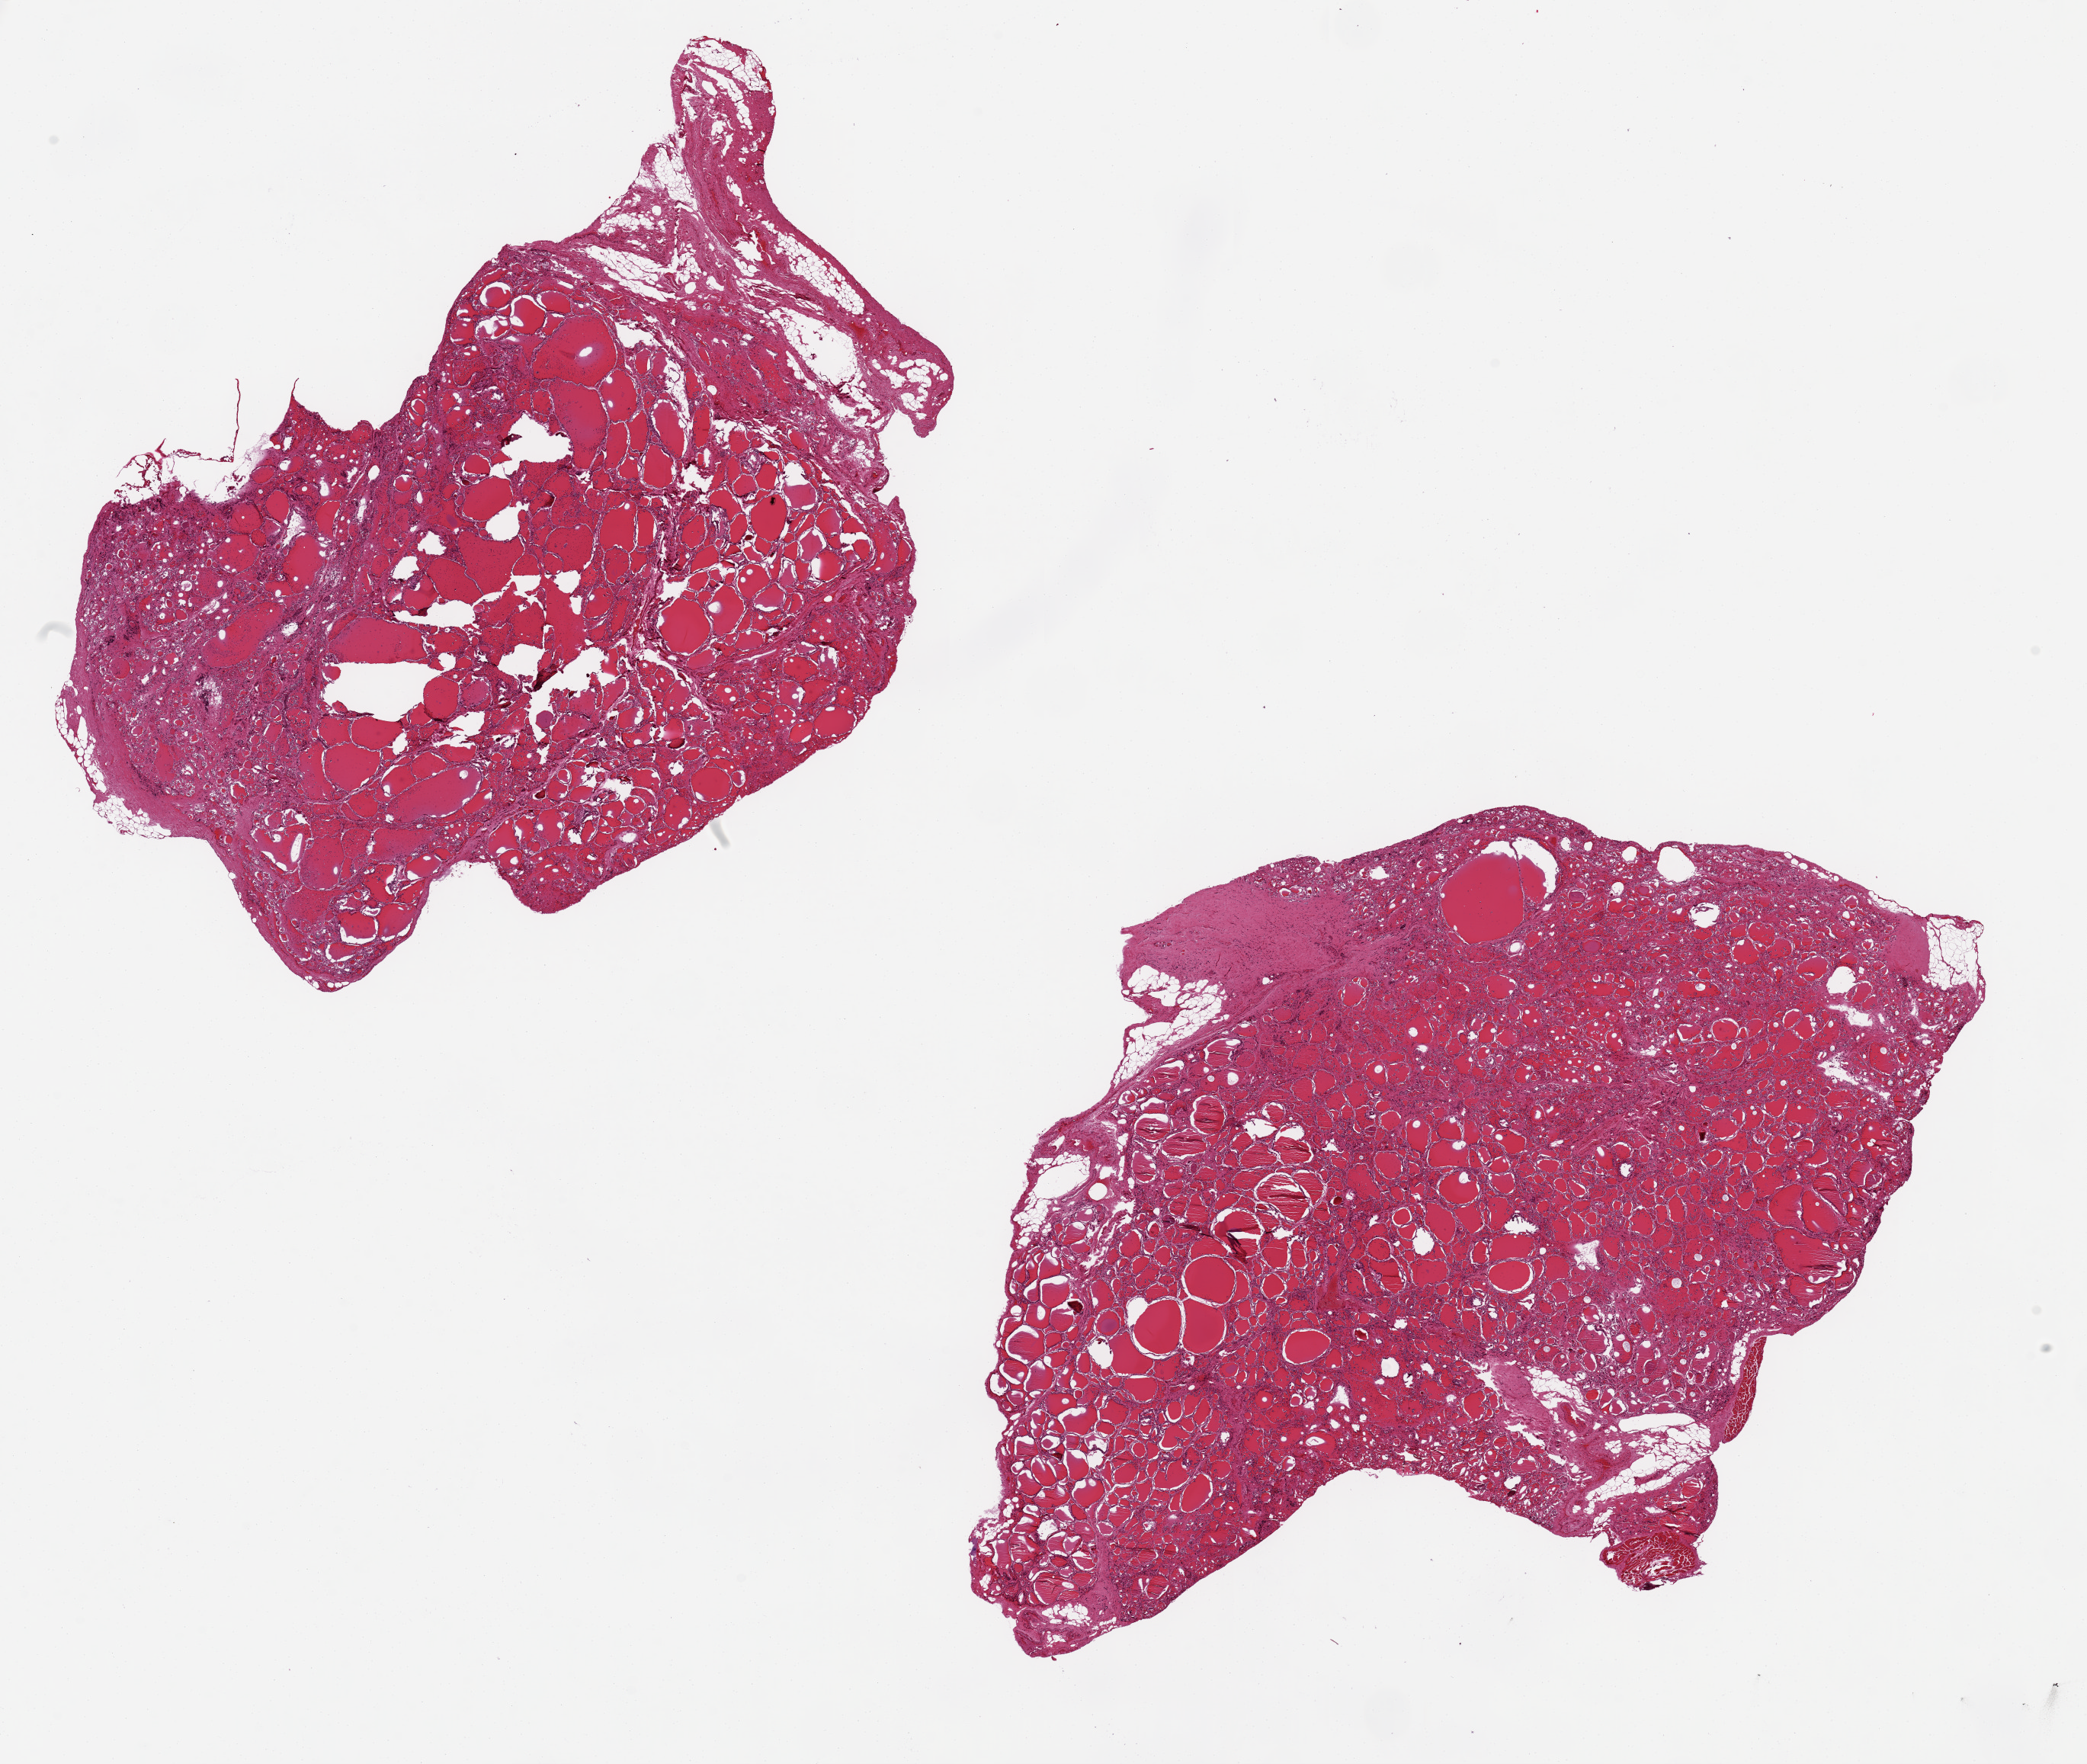
Digitized H&E-stained section — whole scanned area (about 21.7 x 18.3 mm, acquisition: 20x scan) shown as a low-resolution overview. PAXgene-fixed paraffin-embedded (PFPE) section. Target tissue: thyroid. Tissue donor sample. Donor: female.
Pathologist's review note for this sample: 2 aliquots, ~ 8x8mm.